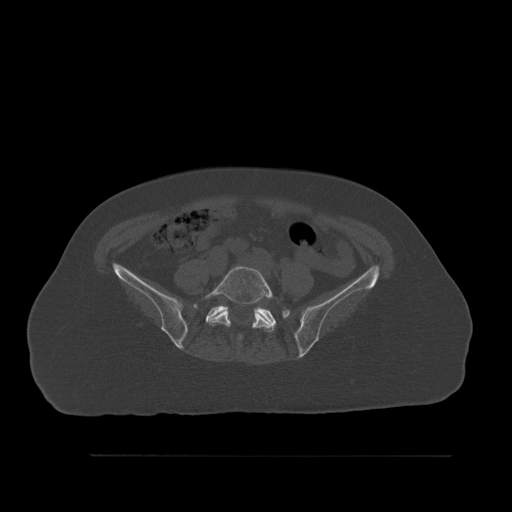
CT including the spine, one axial slice; bone window (W 1800 / L 400 HU); 1.5 mm slice thickness; 512 × 512 image matrix, field of view 470 × 470 mm. Female patient, age 73 years. From the clinical record (not read from this slice): primary cancer: breast; vertebrae with lytic lesions (as recorded): L2.
Annotated regions visible in this slice (semi-automatic segmentation, software-assisted and operator-edited):
- L5 vertebra: bounding box <203,265,278,341> (left, top, right, bottom; pixels)